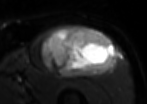
MRI of an extremity soft-tissue mass, one axial slice; position 58 of 85 along the scan axis; T2-weighted fat-saturated; MR volume resampled by the dataset authors to the PET/CT grid (not the native acquisition matrix); 3.27 mm slice thickness; 147 × 104 image matrix, field of view 144 × 102 mm. Male patient. From the clinical record (not read from this slice): histological type: extraskeletal osteosarcoma; grade: high; site of the primary tumour: thigh.
Structures marked on this image (expert contour drawn on MRI and transferred to this co-registered scan by the dataset authors):
- gross tumour volume (mass): bounding box <40,26,116,77> (left, top, right, bottom; pixels)